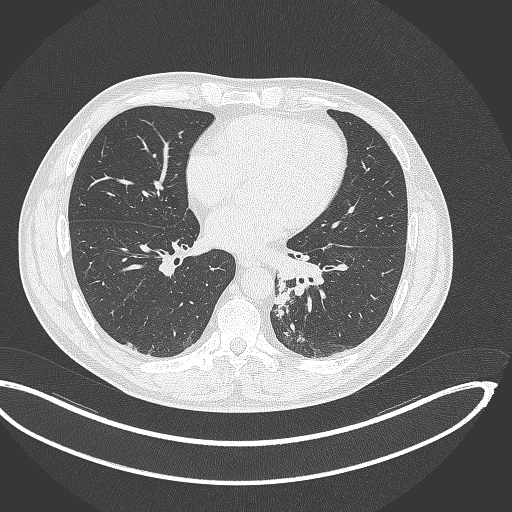
Chest CT, one axial slice. Slice 147 of 362 in the series (ordered by position). 120 kVp. Lung window (W 1500 / L -600 HU). 1 mm slice thickness. 512 × 512 image matrix, field of view 442 × 442 mm. Male patient, age 50 years. Case-level facts recorded for this patient, not image findings: clinical TNM (as recorded): T2a N3 M0.
Structures marked on this image (rectangle marked by the reading radiologist):
- lung tumour (recorded histology: squamous cell carcinoma): bounding box [x1, y1, x2, y2] px = [273, 279, 293, 317]